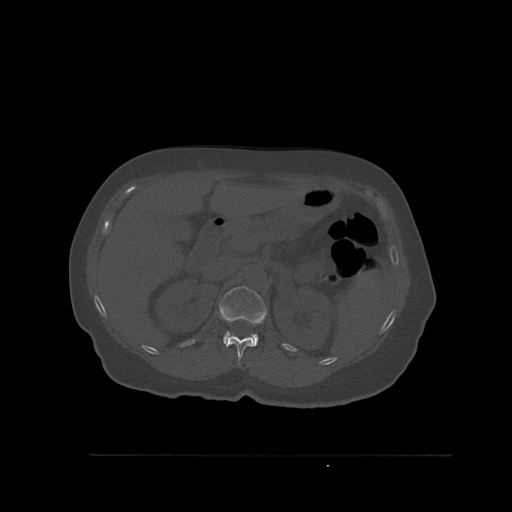
CT including the spine, one axial slice. Position 277 of 527 along the scan axis. Bone window (W 1800 / L 400 HU). 1.5 mm slice thickness. 512 × 512 image matrix. Female patient, age 73 years. From the clinical record (not read from this slice): primary cancer: breast.
Annotated regions visible in this slice (semi-automatically segmented with operator editing):
- L1 vertebra: bounding box [x1, y1, x2, y2] px = [218, 286, 267, 347]
- T12 vertebra: [226, 335, 254, 365]